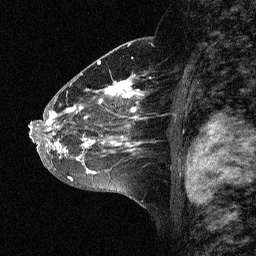
Breast MRI (dynamic contrast-enhanced), one sagittal slice; dynamic contrast-enhanced study with each time point stored as its own series, time point 2 of 3 at this slice position (early post-contrast, ordered by acquisition time); 1.5 T; TE 4.5 ms, TR 11 ms; 2.06 mm slice thickness; 256 × 256 image matrix, field of view 200 × 200 mm. Female patient, age 46 years. From the clinical record (not read from this slice): setting: breast cancer imaged before/during neoadjuvant chemotherapy; receptor status: HER2-positive.
Structures marked on this image (semi-automatic segmentation, software-assisted and operator-edited):
- analysis volume of interest (the breast-tissue region the enhancement analysis was run in; not a lesion): bounding box [x1, y1, x2, y2] px = [43, 72, 164, 177]
- tumour enhancement mask (voxels above the 90 % enhancement threshold inside the analysis volume of interest): [46, 72, 152, 177]